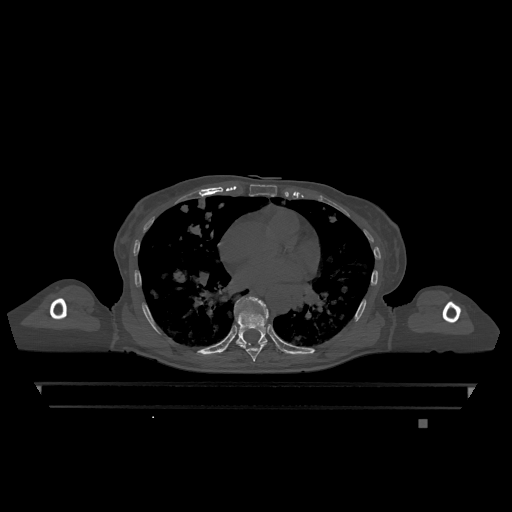
CT including the spine, one axial slice. Bone window (W 1800 / L 400 HU). 0.5 mm slice thickness. 512 × 512 image matrix. Patient: female, 74 years. Case-level facts recorded for this patient, not image findings: primary cancer: lung.
Outlined on this slice (semi-automatic segmentation, software-assisted and operator-edited):
- T7 vertebra: bounding box [x1, y1, x2, y2] px = [239, 344, 267, 362]
- T9 vertebra: [234, 297, 269, 346]